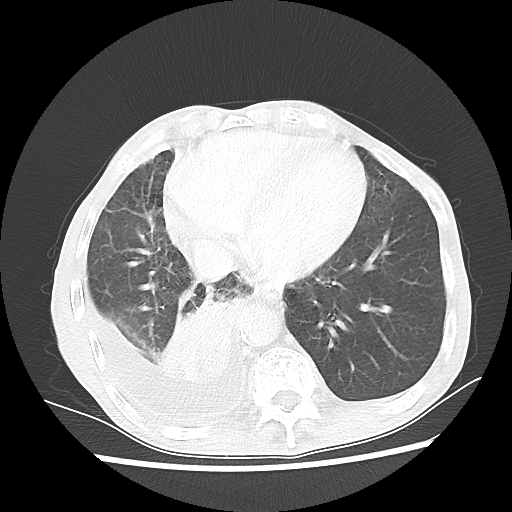
Chest CT, one axial slice; position 19 of 60 along the scan axis; reconstruction kernel LUNG; 80 kVp; lung window (W 1500 / L -600 HU); 5 mm slice thickness; 512 × 512 image matrix, field of view 335 × 335 mm. Male patient, age 76 years. Case-level facts recorded for this patient, not image findings: clinical TNM (as recorded): T3 N3 M1a.
Annotated regions visible in this slice (rectangle marked by the reading radiologist):
- lung tumour (recorded histology: squamous cell carcinoma): box from (x=155, y=282) to (x=241, y=385) px